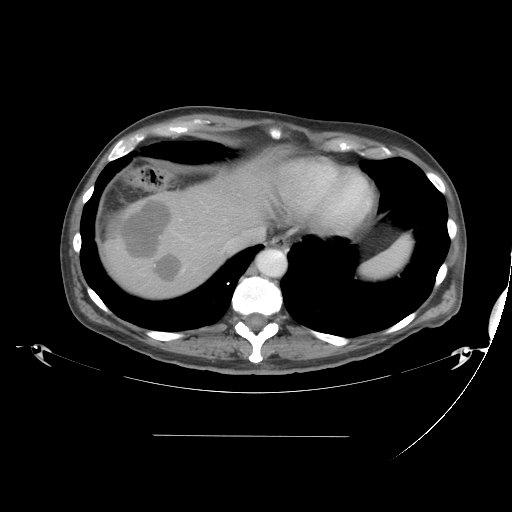
Contrast-enhanced abdominal CT, one axial slice; slice 37 of 48 in the series (ordered by position); 120 kVp; intravenous contrast given; soft-tissue window (W 400 / L 40 HU); 5 mm slice thickness; 512 × 512 image matrix, field of view 486 × 486 mm. Male patient, age 65 years. From the clinical record (not read from this slice): diagnosis: colorectal cancer liver metastases, imaged before liver resection; multiple liver metastases: yes; largest metastasis: 11 cm; disease in both lobes: yes.
Annotated regions visible in this slice (expert manual segmentation):
- hepatic veins: bounding box (x1, y1, x2, y2) in pixels: (170, 227, 264, 250)
- liver: (102, 164, 270, 301)
- planned liver remnant (the part of the liver to remain after resection): (190, 164, 272, 234)
- portal vein (with intrahepatic branches): (184, 201, 226, 228)
- liver metastasis: (155, 256, 181, 280)
- liver metastasis: (116, 200, 171, 259)